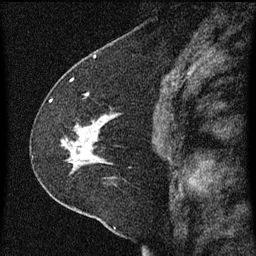
Breast MRI (dynamic contrast-enhanced), one sagittal slice; slice 35 of 60 in the series (ordered by position); dynamic contrast-enhanced series, image 2 of 3 at this slice position (ordered by acquisition); 1.5 T; TE 4.2 ms, TR 8 ms; 256 × 256 image matrix, field of view 180 × 180 mm. Patient: female, 47 years.
Annotated regions visible in this slice (semi-automatic segmentation, software-assisted and operator-edited):
- analysis volume of interest (the breast-tissue region the enhancement analysis was run in; not a lesion): box from (x=36, y=96) to (x=126, y=213) px
- tumour enhancement mask (voxels above the 70 % enhancement threshold inside the analysis volume of interest): (x=63, y=116)–(x=106, y=167)